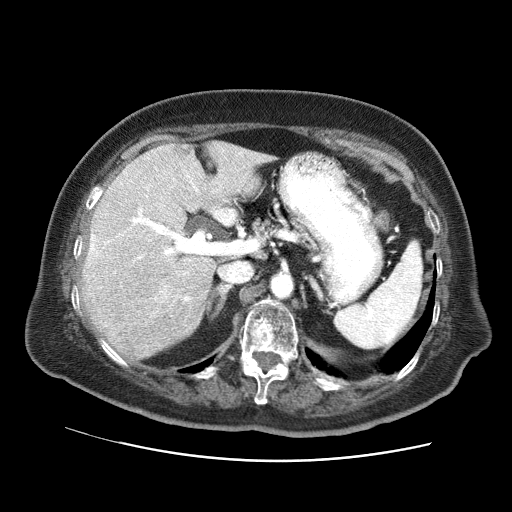
Contrast-enhanced abdominal CT (liver protocol), one axial slice; position 40 of 73 along the scan axis; 120 kVp; soft-tissue window (W 400 / L 40 HU); 512 × 512 image matrix, field of view 380 × 380 mm. Case-level facts recorded for this patient, not image findings: diagnosis: hepatocellular carcinoma (patient treated with transarterial chemoembolisation; whether this scan precedes or follows treatment is not stated here); TNM stage (as recorded): Stage-I; Child-Pugh class: A; tumour differentiation: well differentiated; tumour nodularity: uninodular.
Annotated regions visible in this slice (semi-automatic segmentation, software-assisted and operator-edited):
- liver parenchyma outside the tumour (the mass and vessels are separate outlines, so this box may not span the whole liver): box from (x=82, y=140) to (x=276, y=358) px
- mass: (x=154, y=284)–(x=175, y=306)
- liver vessels: (x=89, y=153)–(x=241, y=302)